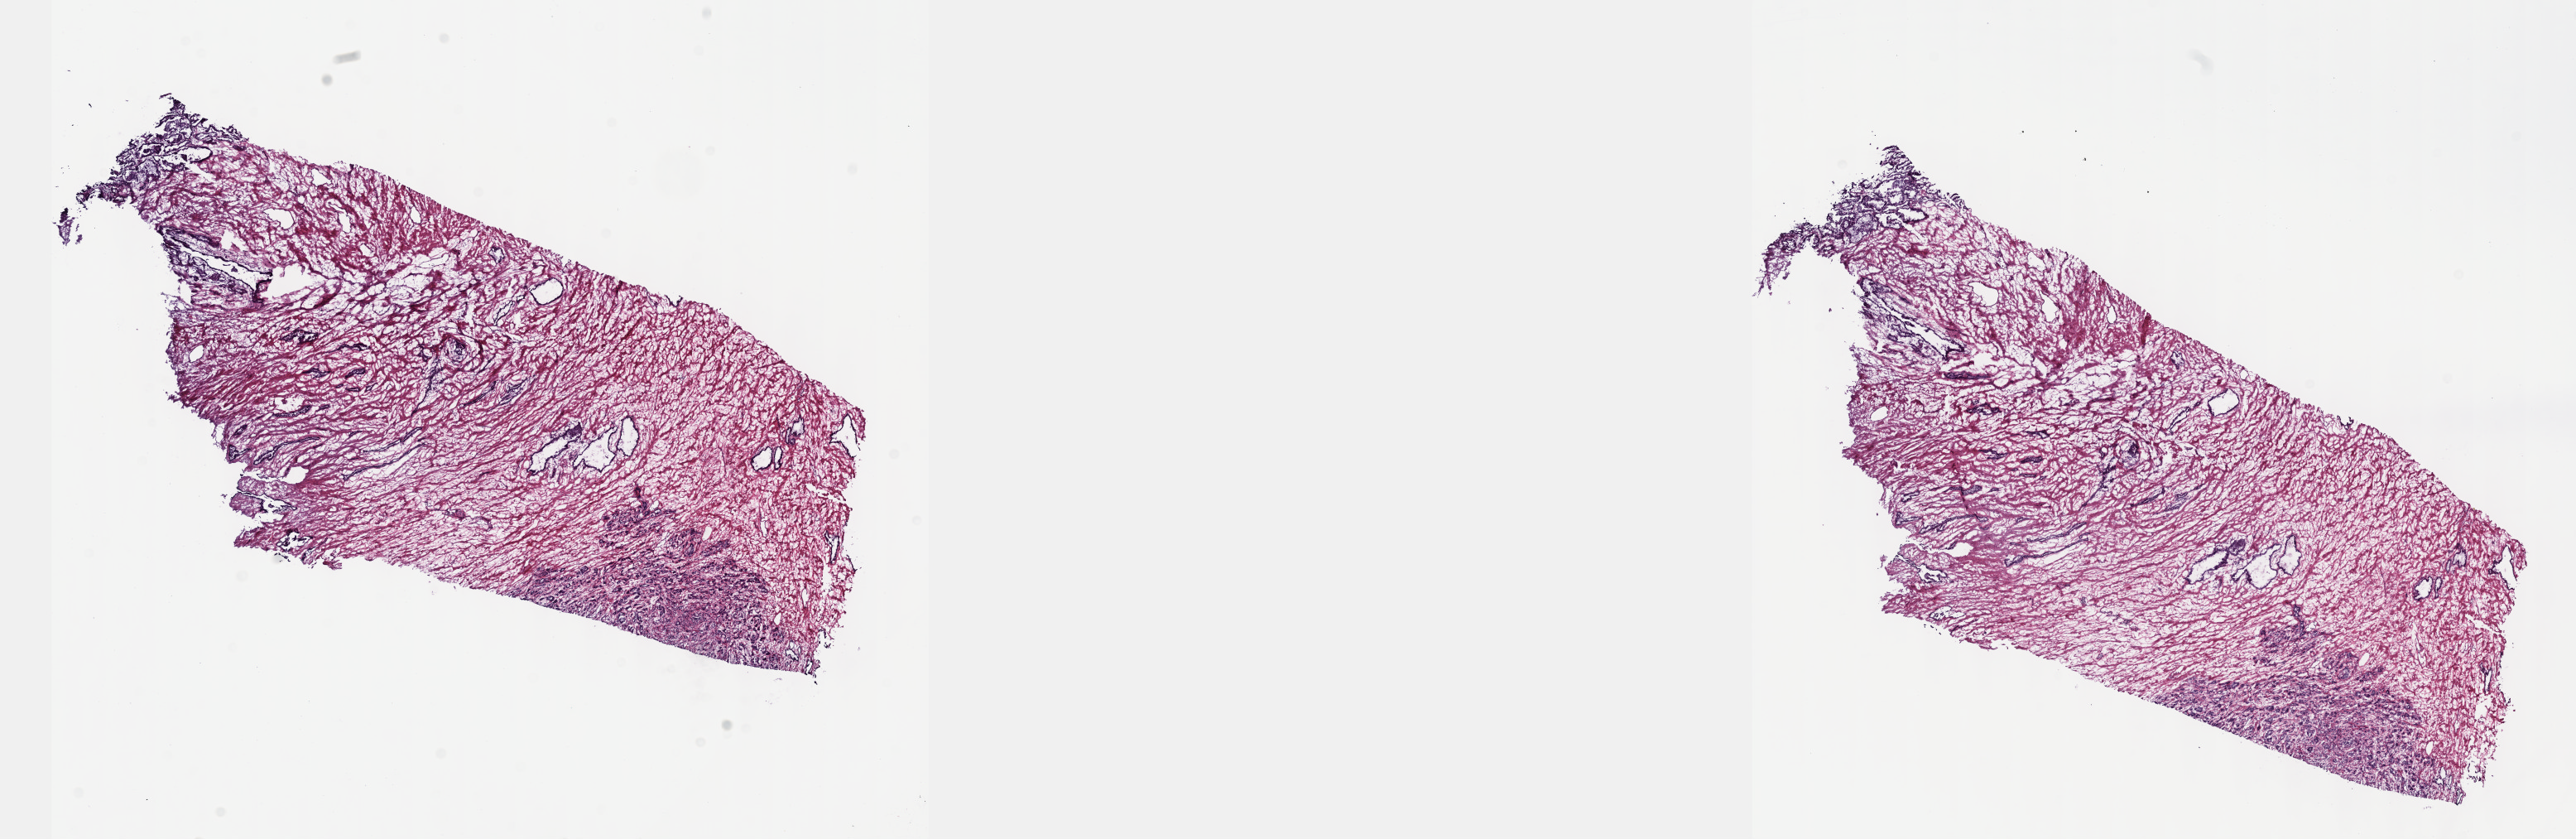
Digitized Hematoxylin and eosin (H&E) stained tissue section (whole slide) — low-resolution overview of the scanned area, about 25.1 x 8.2 mm; frozen section from the top of the tissue portion; primary tumour sample from the prostate. Male, age 64 years at initial diagnosis.
Pathologic diagnosis: Adenocarcinoma, NOS (prostate gland).